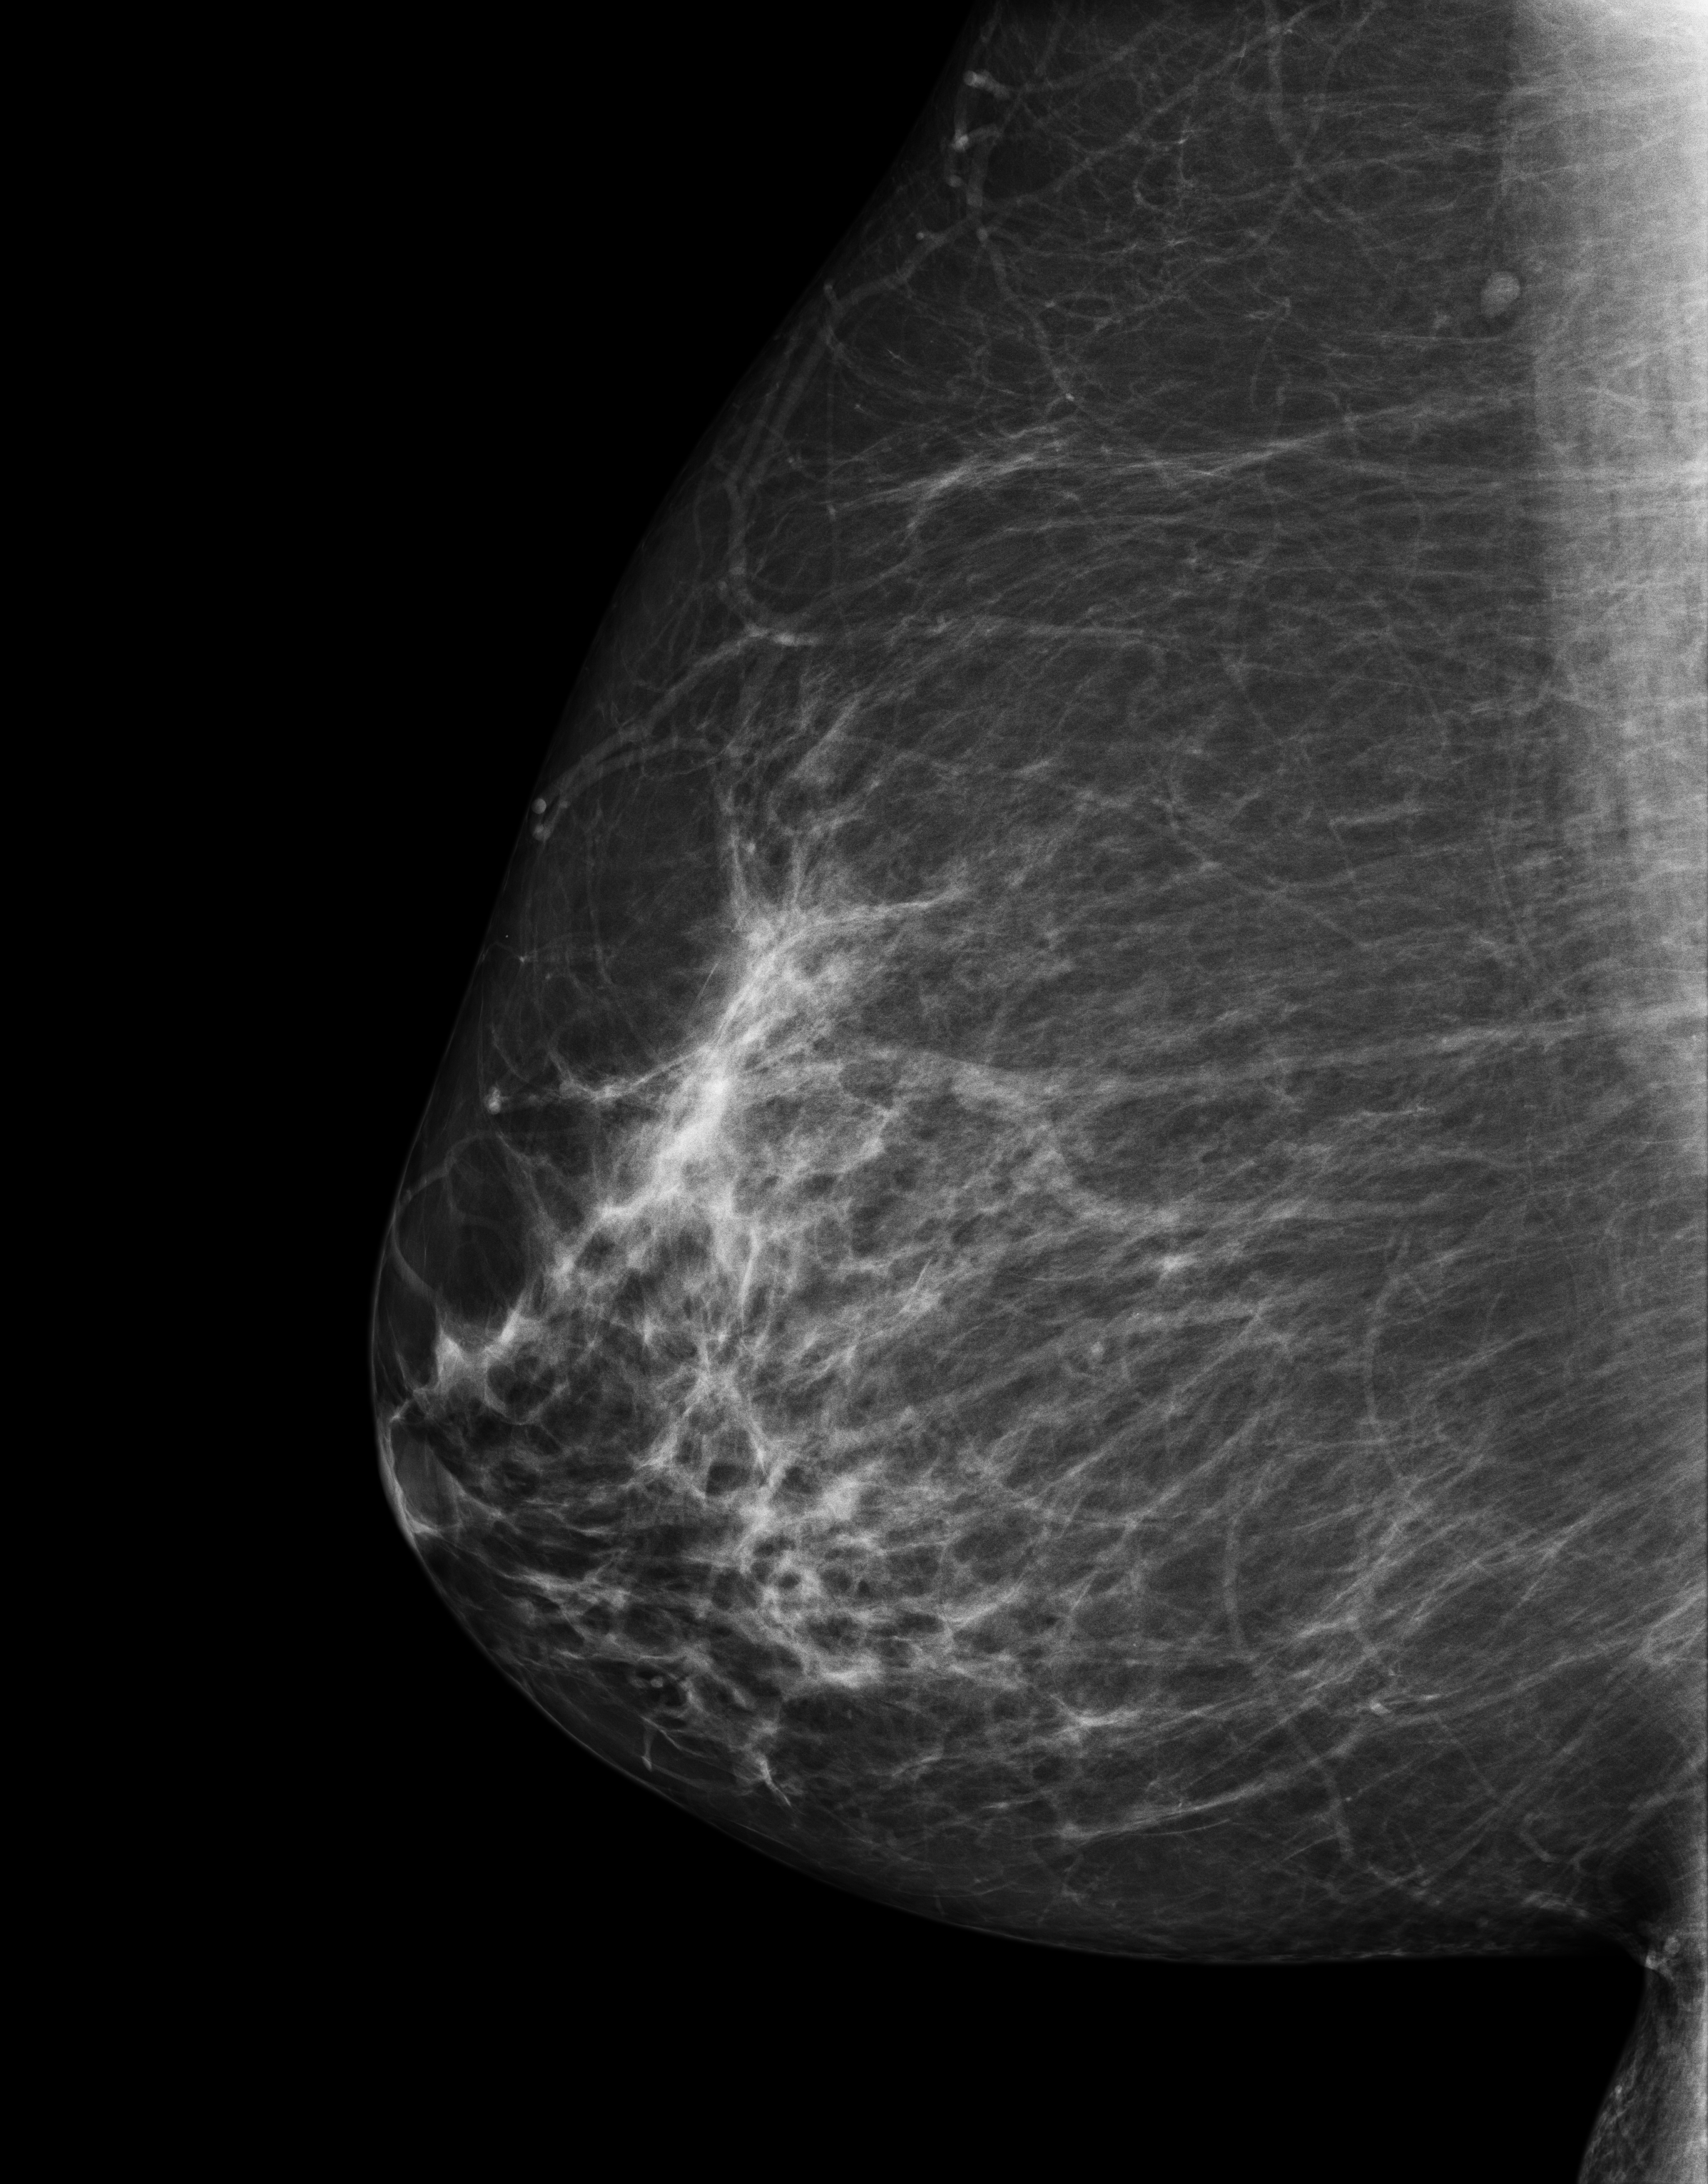
Screening examination. Female patient, age 58 years.
Image type: full-field digital mammogram. Breast: right. Projection: mediolateral oblique (MLO) view.